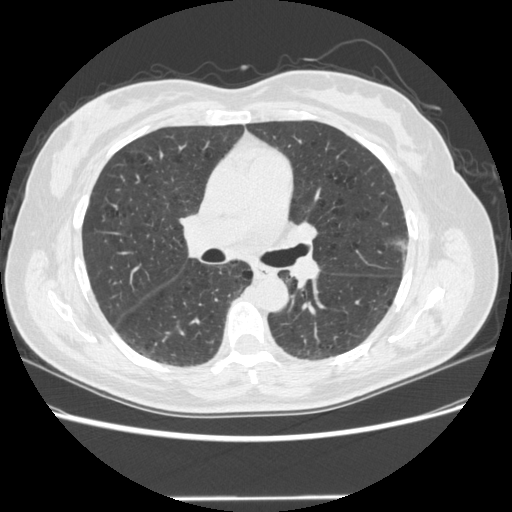
Low-dose screening chest CT, axial slice, baseline screening round, lung window (W 1500 / L -600 HU), 1.25 mm slice thickness, 120 kVp, slice 184 of 301 in the series, 512 × 512 image matrix. Female, age 61 years at enrolment.
Lesion marked by an expert reader, bounding box <383,228,428,278> (left, top, right, bottom; pixels). Screening reader's record for this exam: no non-calcified nodule ≥4 mm recorded. Lung cancer was diagnosed 791 days after this screen: bronchiolo-alveolar adenocarcinoma, NOS, left upper lobe, well differentiated (G1), stage IA (AJCC 6th edition), 11 mm at pathology.